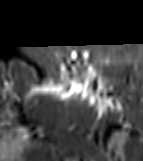
MRI of an extremity soft-tissue mass, one axial slice; slice 51 of 81 in the series (ordered by position); STIR; MR volume resampled by the dataset authors to the PET/CT grid (not the native acquisition matrix); 3.27 mm slice thickness; 143 × 161 image matrix. Female patient. Case-level facts recorded for this patient, not image findings: histological type: myxofibrosarcoma; grade: intermediate; site of the primary tumour: left thigh.
Outlined on this slice (expert contour drawn on MRI and transferred to this co-registered scan by the dataset authors):
- gross tumour volume including surrounding oedema: bounding box (x1, y1, x2, y2) in pixels: (28, 69, 116, 107)